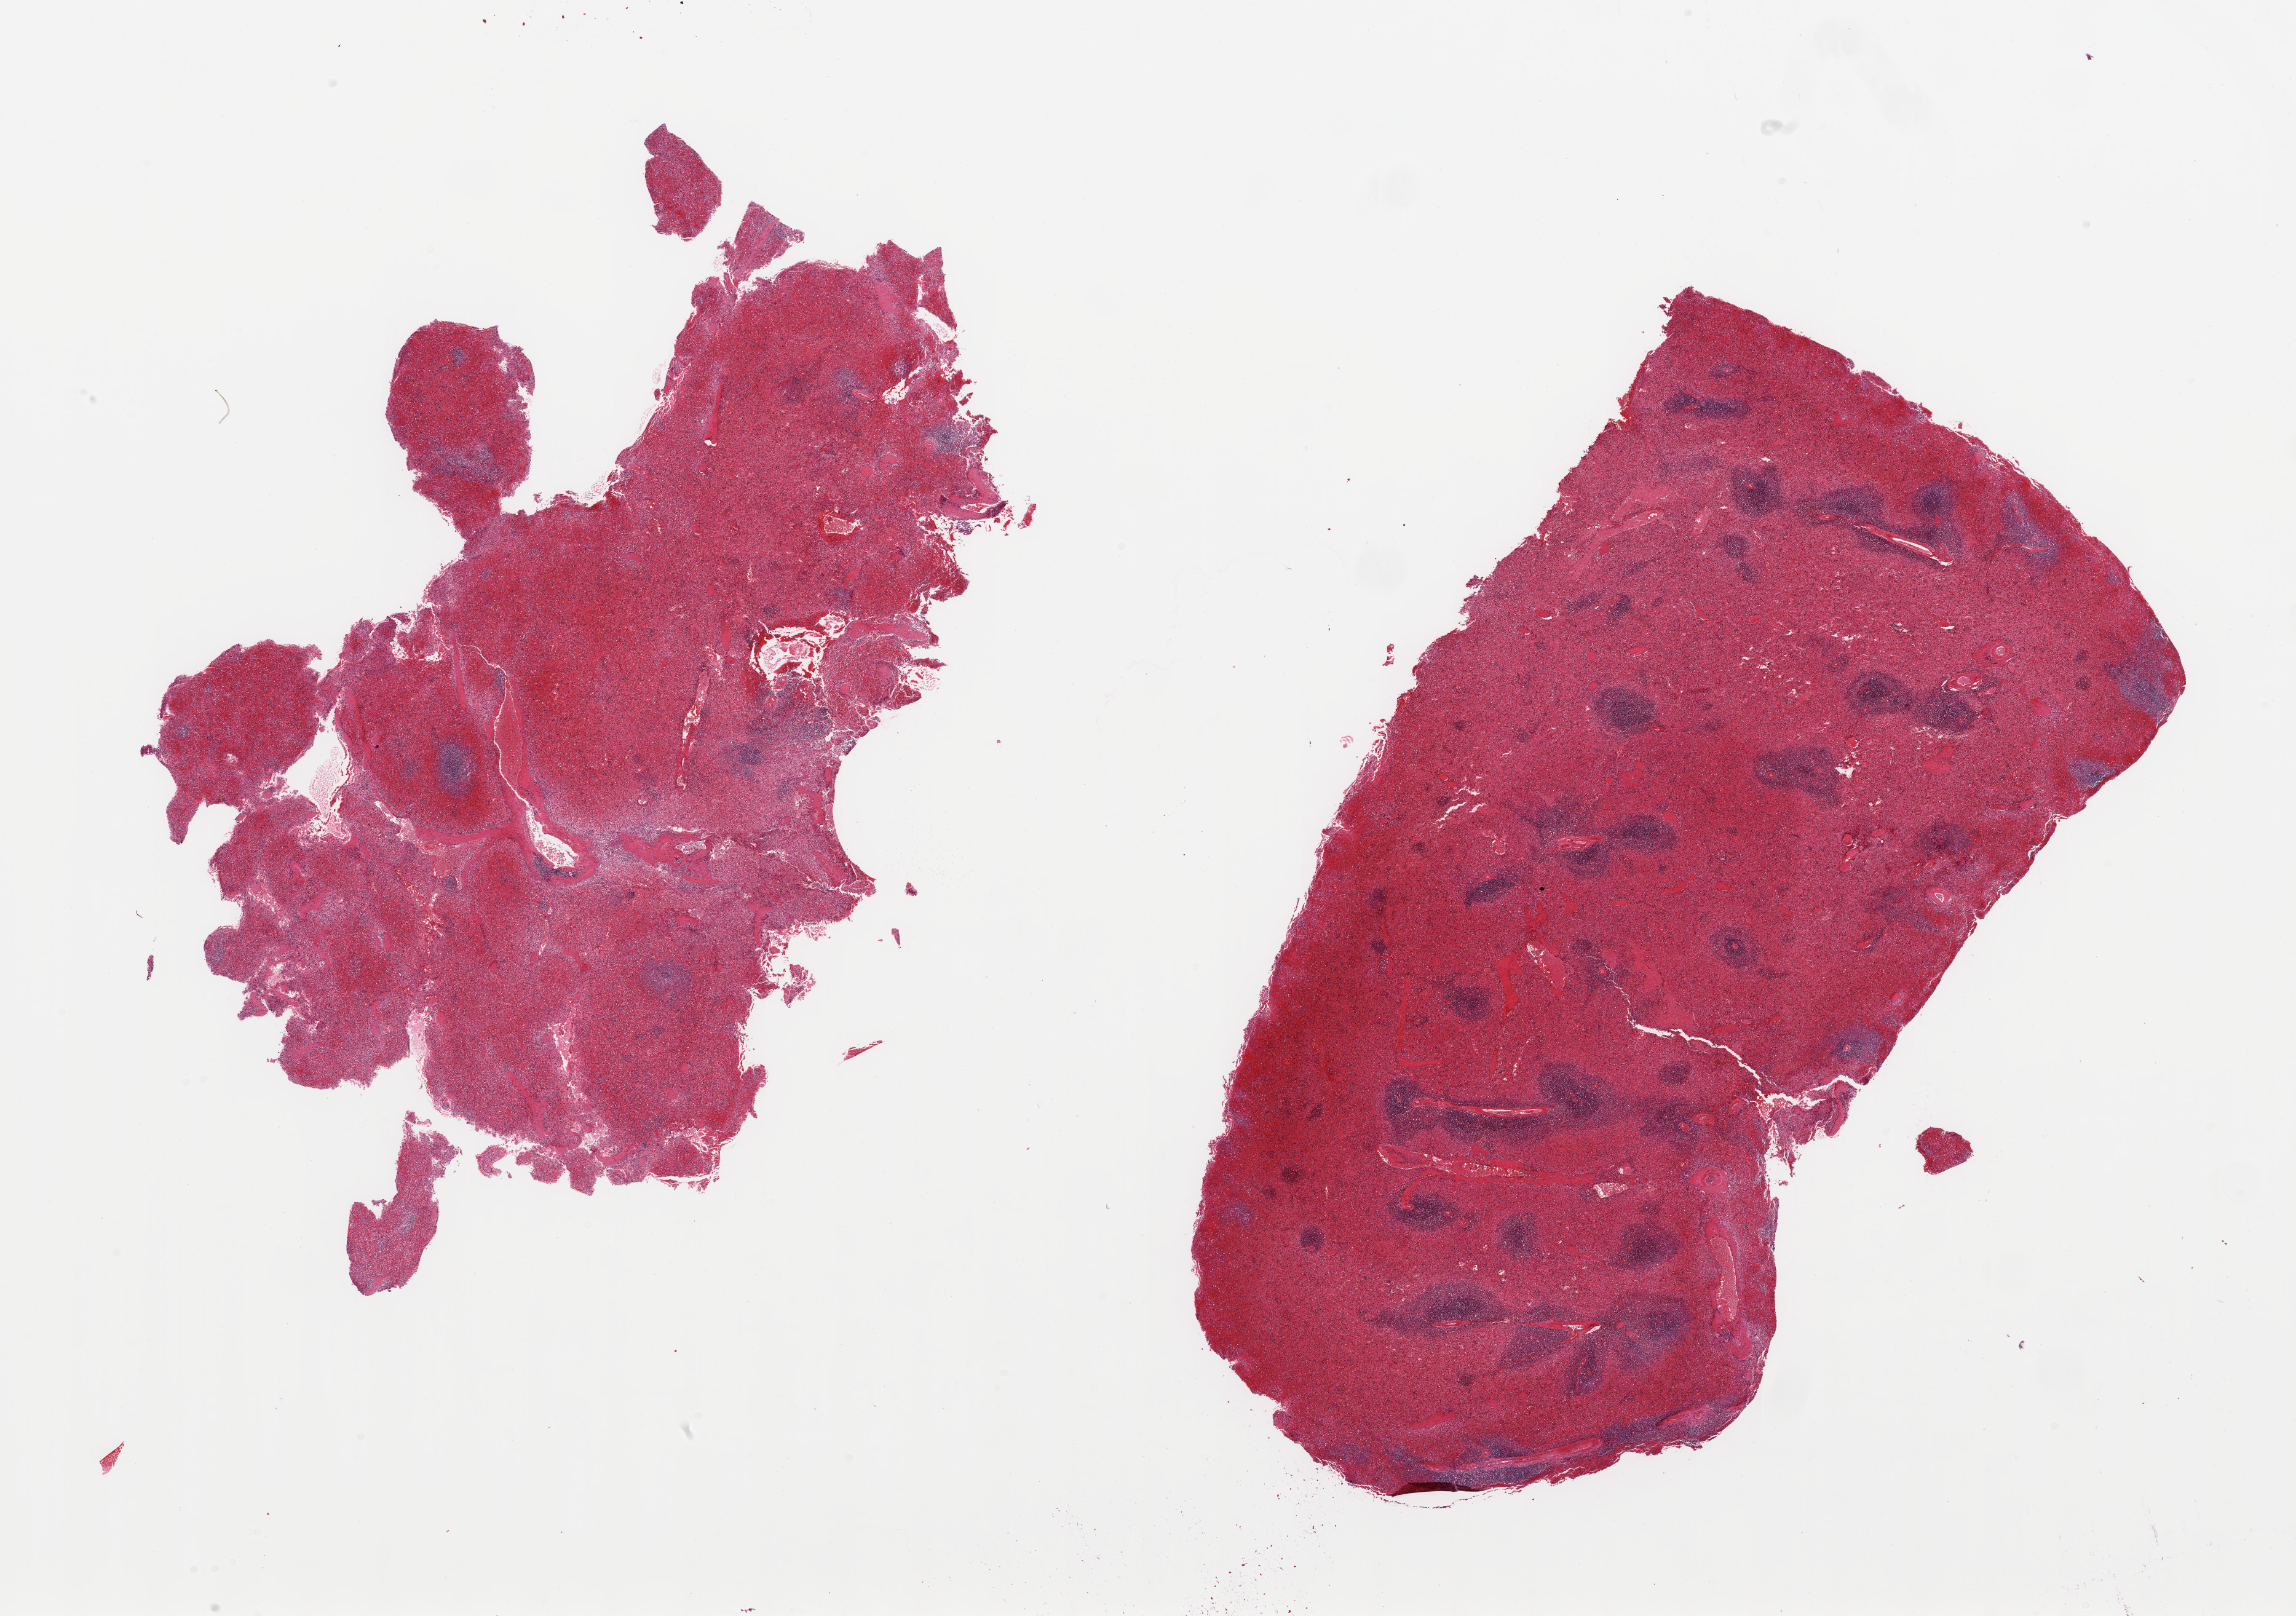
Hematoxylin and eosin (H&E) whole-slide image, low-resolution overview of the scanned area, about 29.5 x 20.8 mm (slide scanned at 20x). PAXgene-fixed paraffin-embedded (PFPE) section. Target tissue: spleen. Donor tissue sample. Male donor.
* reviewer comment on this tissue sample: 2 pieces, moderate congestion